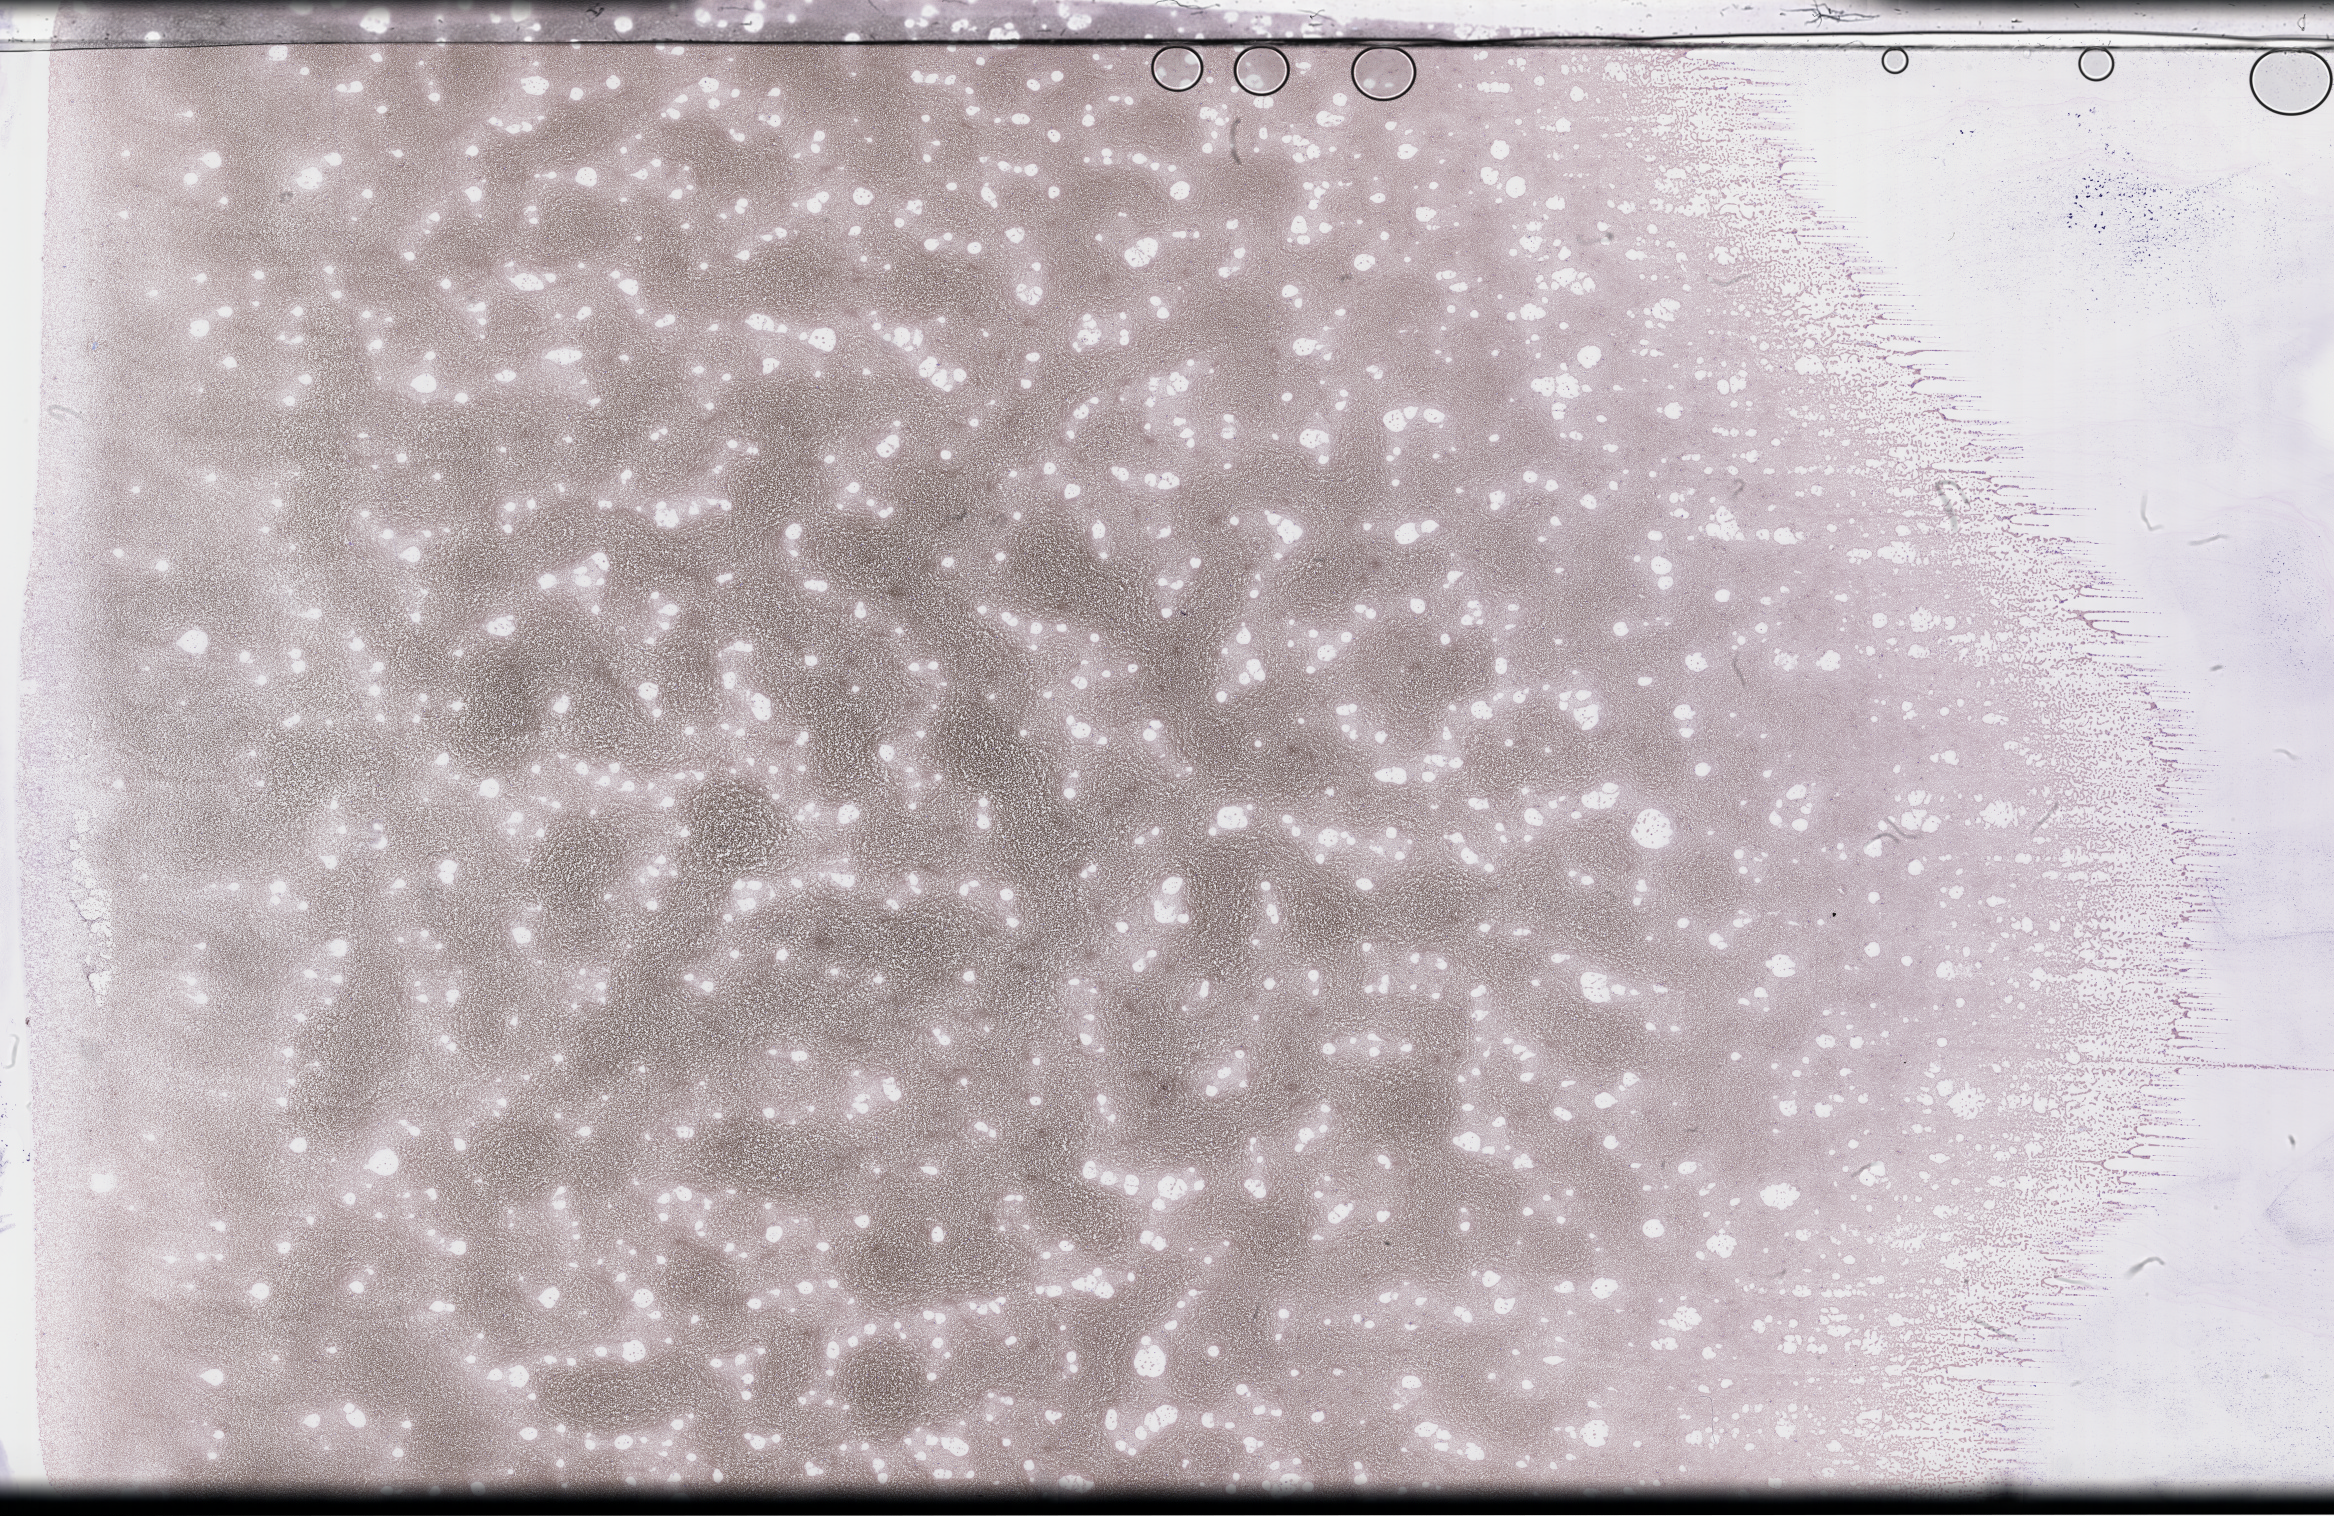
Wright–Giemsa-stained whole blood smear, whole-slide image, low-resolution overview of the scanned area, about 37.7 x 24.5 mm, collected on treatment. Patient: female.
* patient diagnosis: Plasma Cell Myeloma